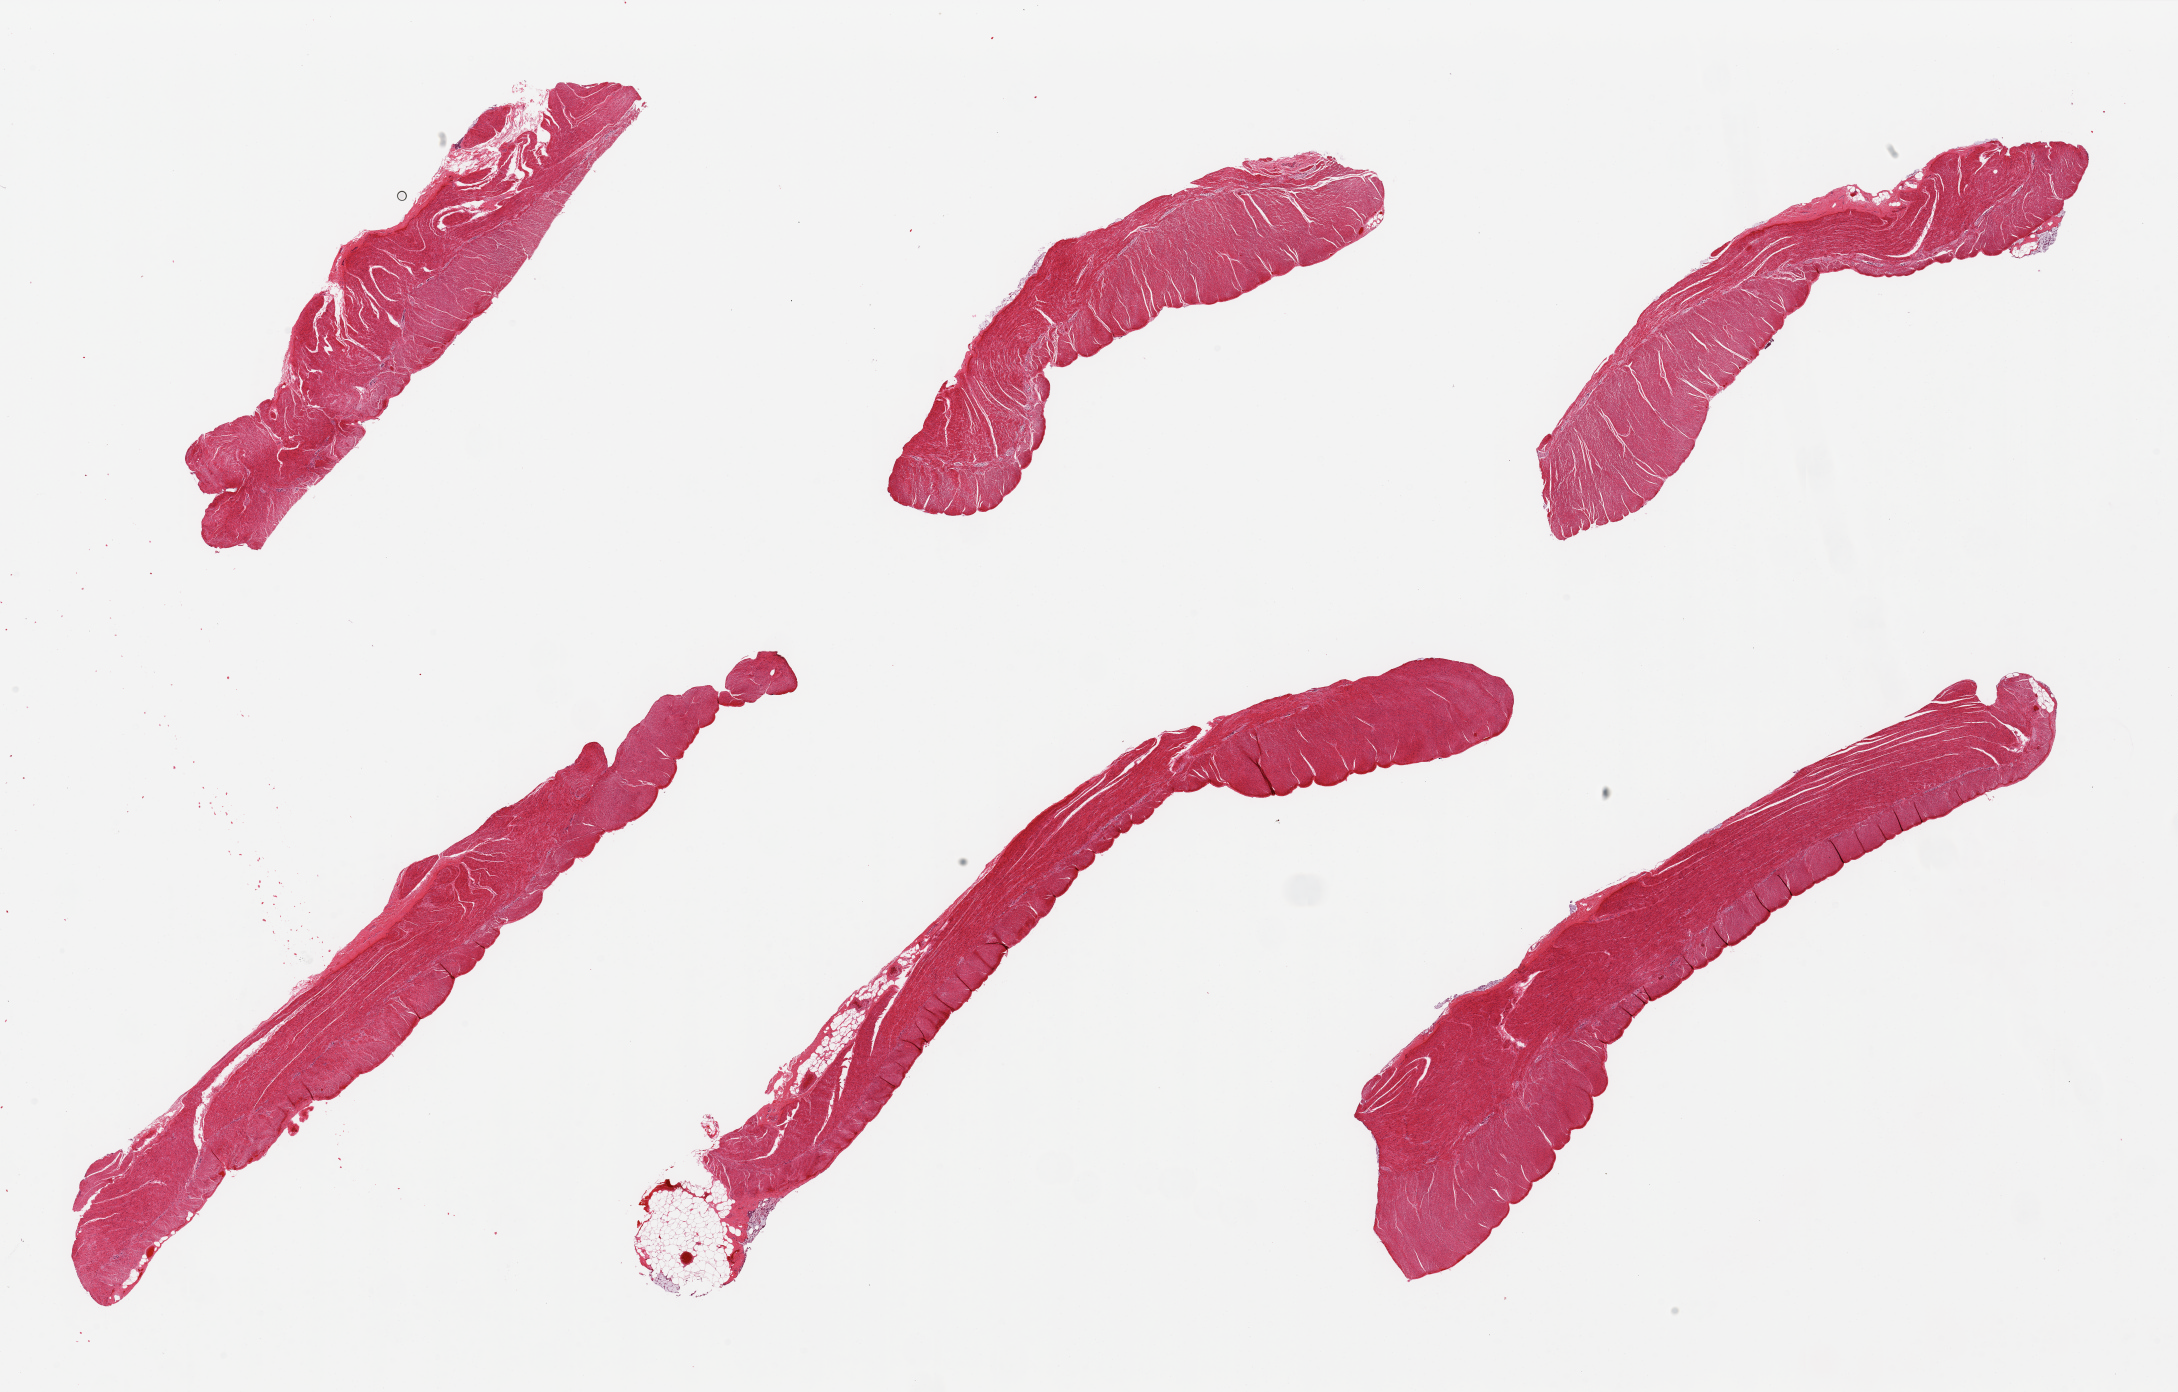
Digitized haematoxylin and eosin-stained section — shown as a low-resolution overview of the whole scanned area (about 34.5 x 22.0 mm, slide scanned at 20x). PAXgene-fixed, paraffin-embedded tissue. Target tissue: sigmoid colon. Tissue donor sample. Male donor.
• reviewer comment on this tissue sample: 6 pieces; well dissected muscle, virtually free of fat